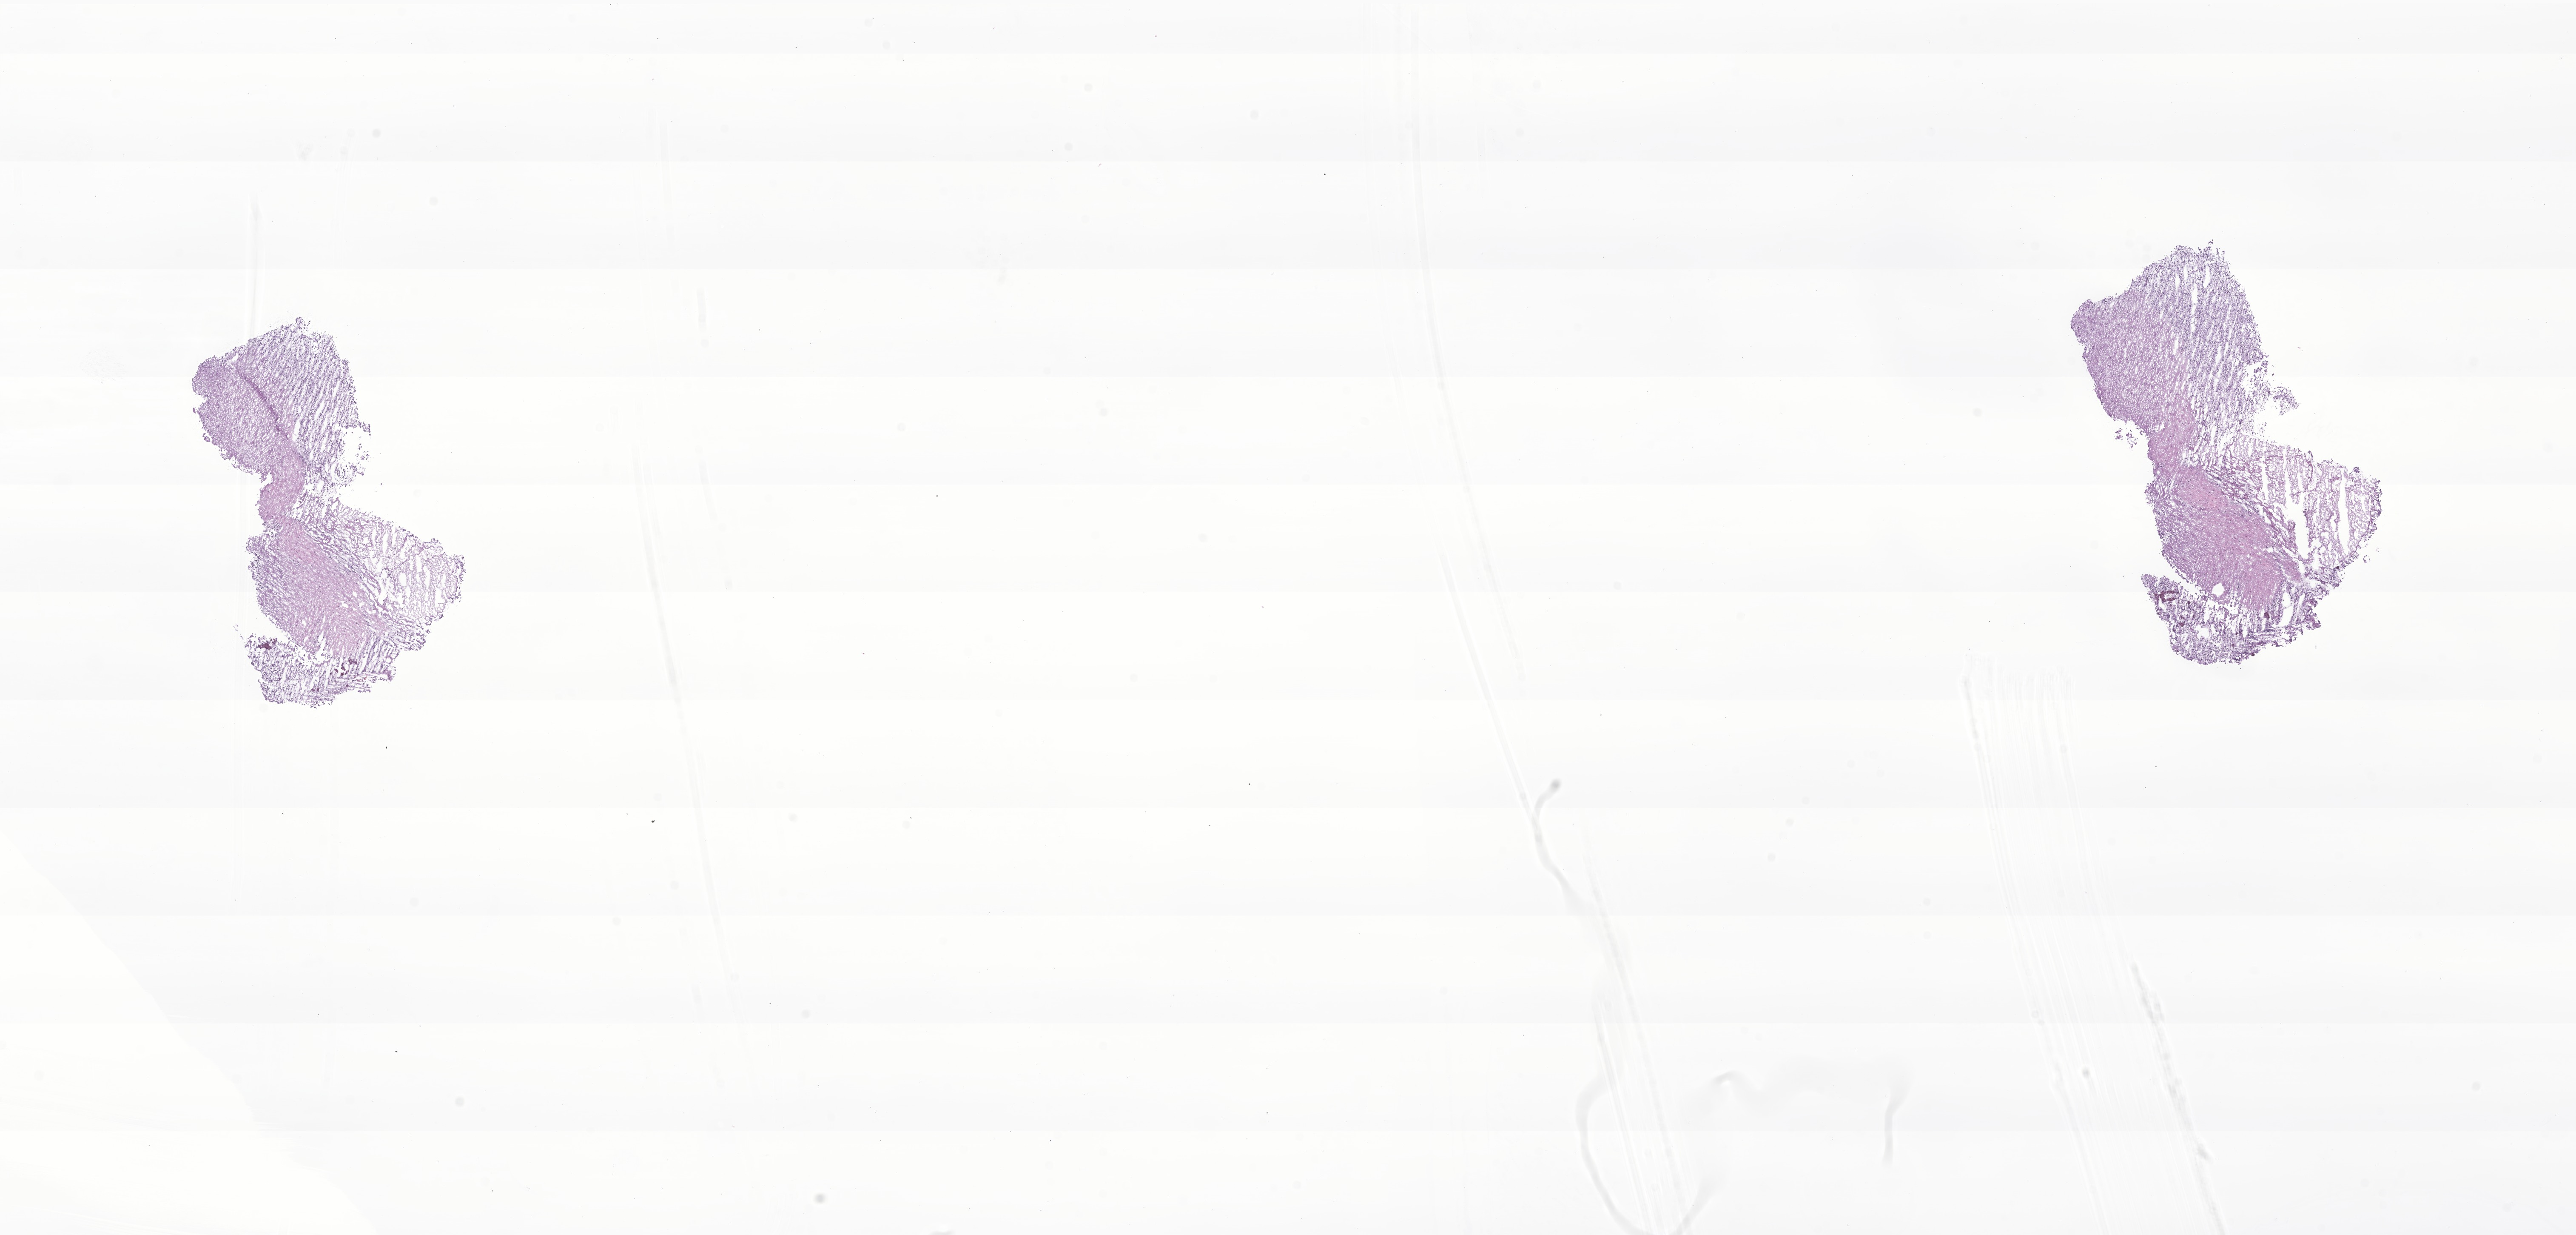
Haematoxylin and eosin whole-slide image of tumor tissue from the brain — shown as a low-resolution overview of the whole scanned area (about 25.5 x 12.2 mm), cryosection (OCT / tissue freezing medium). Male patient, age 125 months (10 years 5 months).
• diagnosis: Glioma, malignant